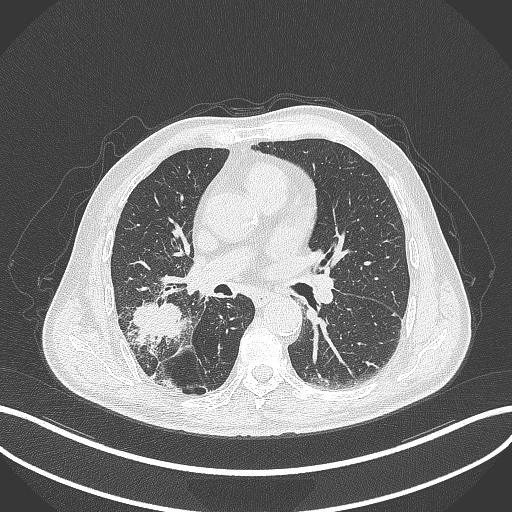
Chest CT, one axial slice. Reconstruction kernel B70f. 120 kVp. Lung window (W 1500 / L -600 HU). 1 mm slice thickness. 512 × 512 image matrix, field of view 400 × 400 mm. Patient: male, 72 years. From the clinical record (not read from this slice): clinical TNM (as recorded): T3 N2 M0.
Annotated regions visible in this slice (rectangle marked by the reading radiologist):
- lung tumour (recorded histology: adenocarcinoma): bounding box <126,297,189,351> (left, top, right, bottom; pixels)